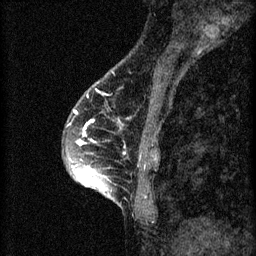
Breast MRI (dynamic contrast-enhanced), one sagittal slice. Position 22 of 60 along the scan axis. 3 images stored at this slice position (order not interpretable as contrast timing). 1.5 T. TE 4.2 ms, TR 8.2 ms. 256 × 256 image matrix, field of view 180 × 180 mm. Female patient, age 45 years.
Outlined on this slice (semi-automatic segmentation, software-assisted and operator-edited):
- analysis volume of interest (the breast-tissue region the enhancement analysis was run in; not a lesion): bounding box <64,104,159,217> (left, top, right, bottom; pixels)
- tumour enhancement mask (voxels above the 70 % enhancement threshold inside the analysis volume of interest): <70,110,125,197>